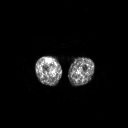
FDG PET of an extremity soft-tissue mass (from a PET/CT study), one axial slice. 3.27 mm slice thickness. 128 × 128 image matrix, field of view 700 × 700 mm. Male patient, age 56 years. From the clinical record (not read from this slice): histological type: pleiomorphic leiomyosarcoma; grade: intermediate; site of the primary tumour: right thigh.
Structures marked on this image (expert contour drawn on MRI and transferred to this co-registered scan by the dataset authors):
- gross tumour volume including surrounding oedema: bounding box <46,59,51,62> (left, top, right, bottom; pixels)